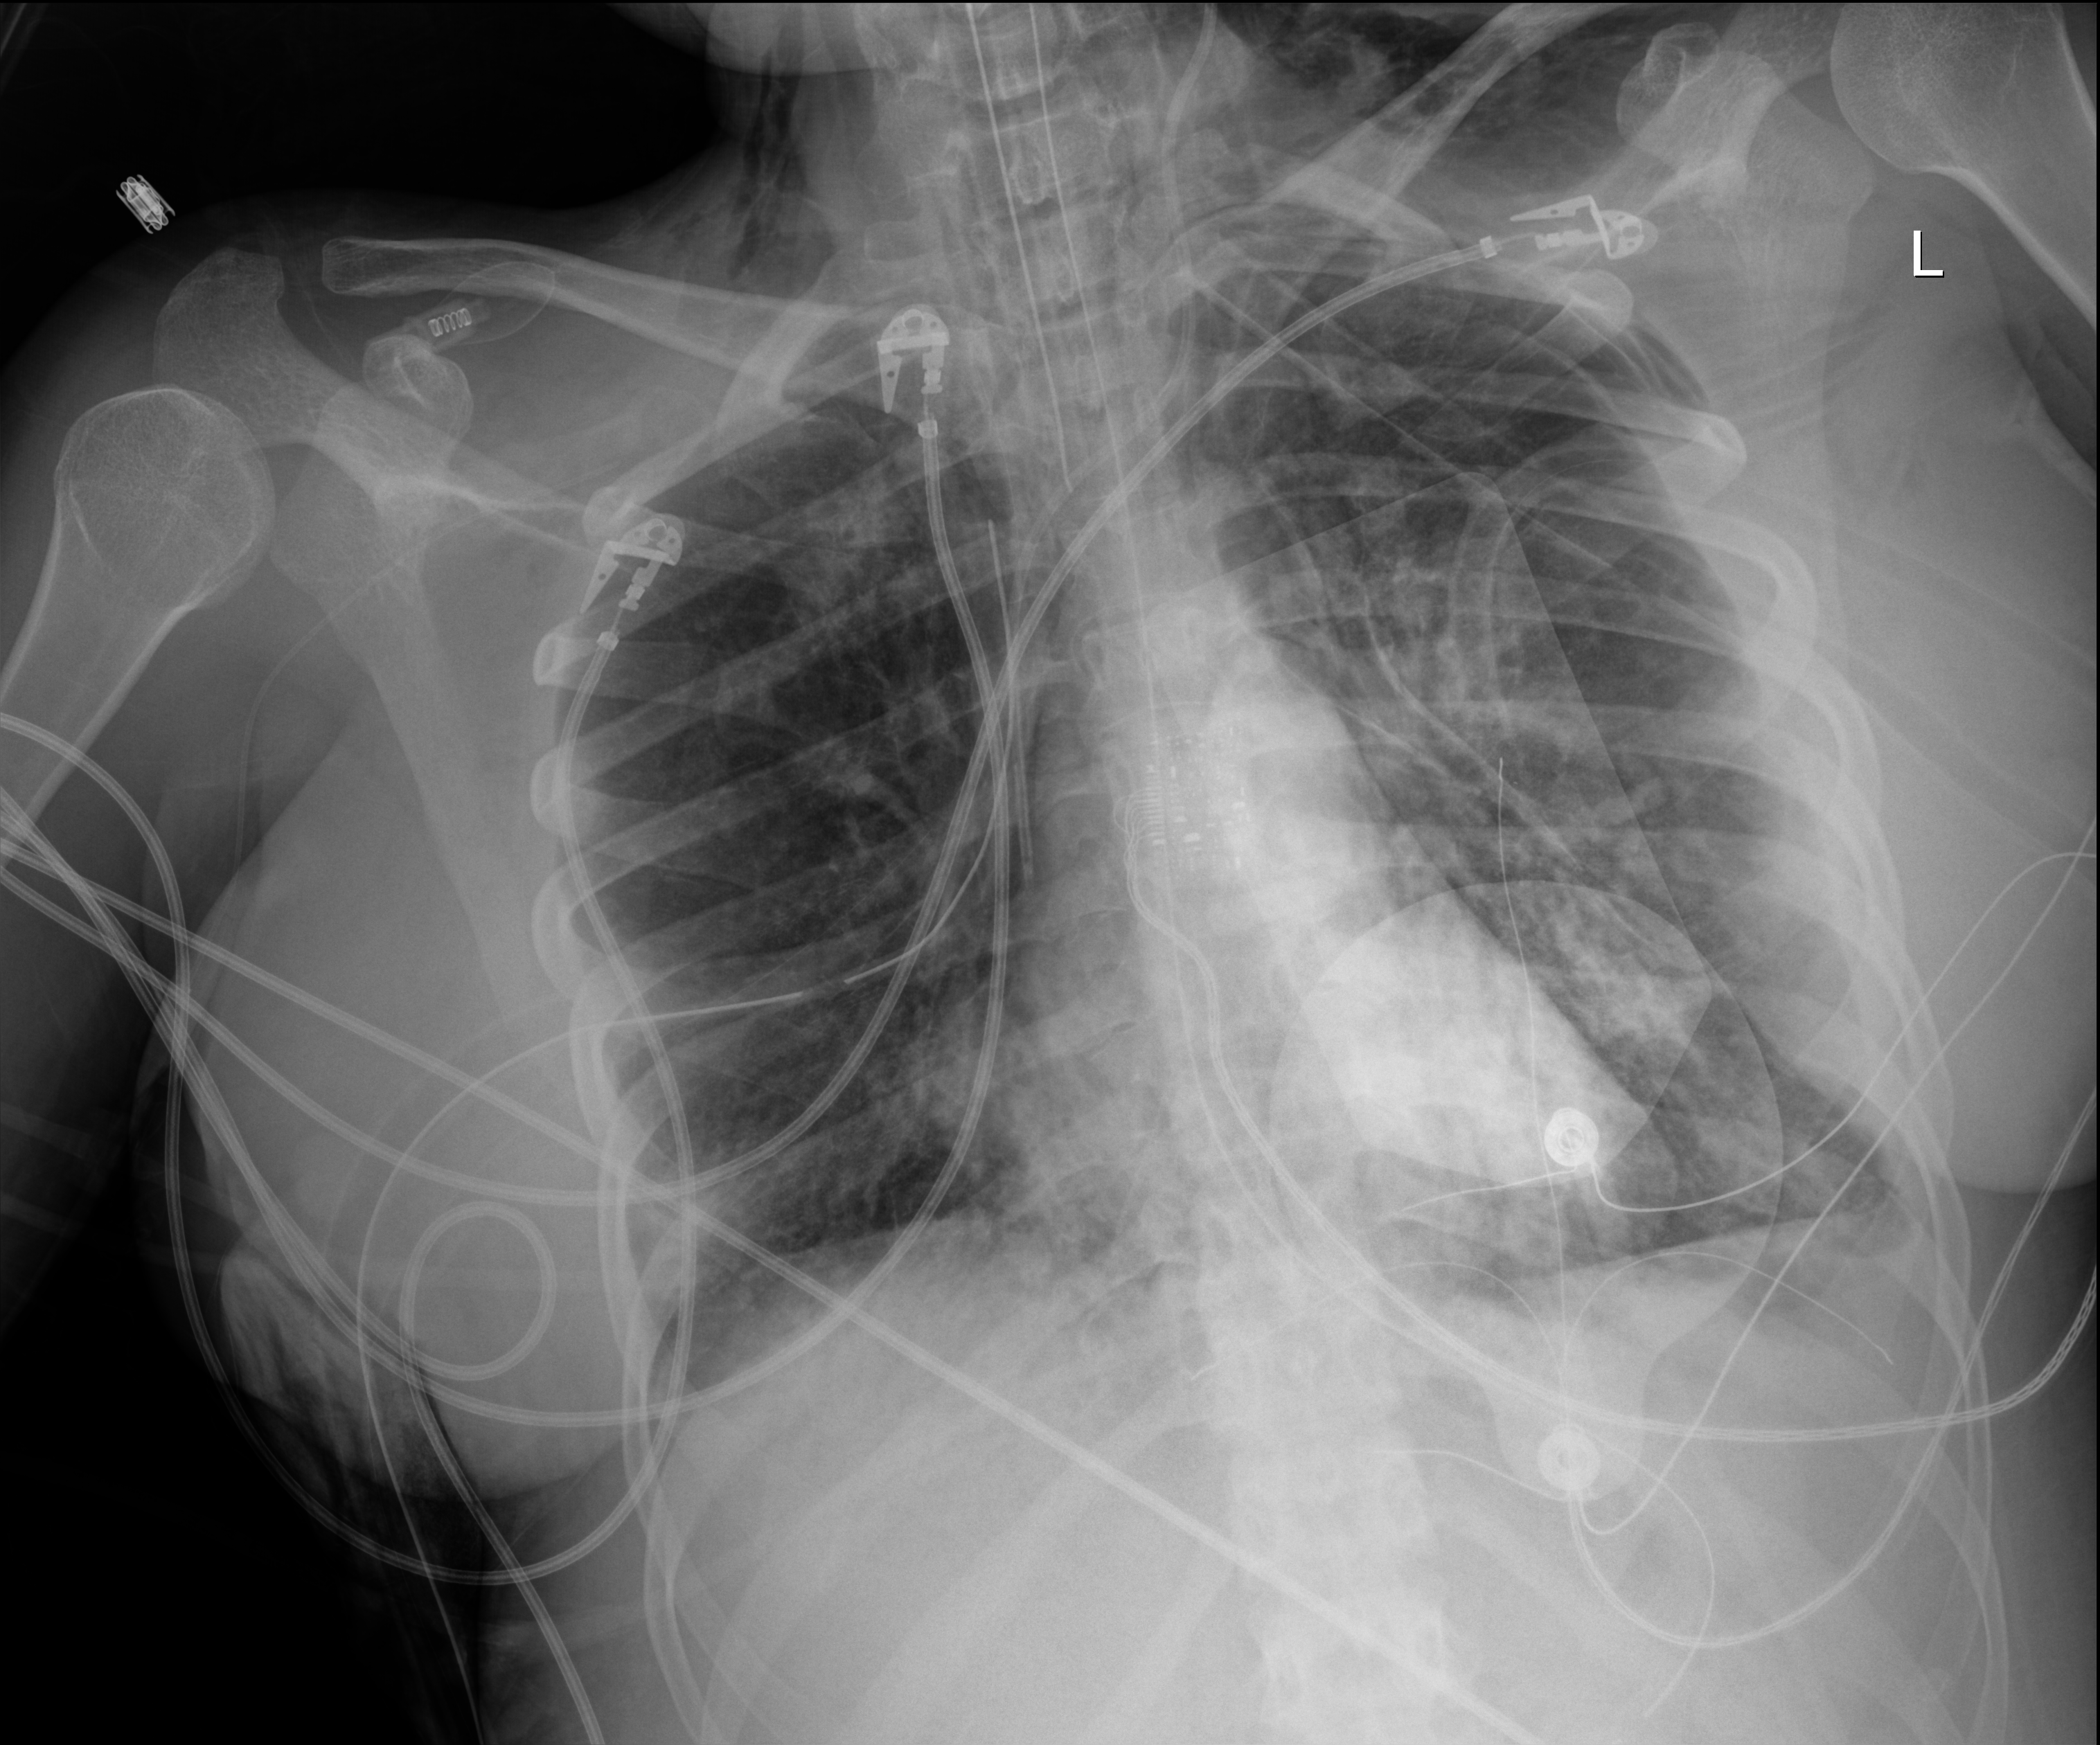
Chest radiograph (digital radiography), anteroposterior (AP) projection. Adult patient hospitalised with COVID-19, age 18–59 years.
Hospital-stay facts (about this admission, not read from this image; timing relative to this image not recorded):
- other chronic lung disease (admission record): no
- mechanically ventilated during this hospital stay: yes